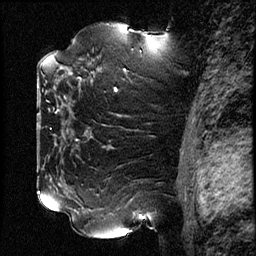
Breast MRI (dynamic contrast-enhanced), one sagittal slice; position 52 of 78 along the scan axis; dynamic contrast-enhanced study with each time point stored as its own series, time point 2 of 3 at this slice position (early post-contrast, ordered by acquisition time); 1.5 T; TE 4.2 ms, TR 17.6 ms; 256 × 256 image matrix, field of view 200 × 200 mm. Female patient, age 42 years. Case-level facts recorded for this patient, not image findings: setting: breast cancer imaged before/during neoadjuvant chemotherapy; receptor status: HER2-positive.
Outlined on this slice (semi-automatic segmentation, software-assisted and operator-edited):
- analysis volume of interest (the breast-tissue region the enhancement analysis was run in; not a lesion): bounding box (x1, y1, x2, y2) in pixels: (50, 48, 131, 129)
- tumour enhancement mask (voxels above the 100 % enhancement threshold inside the analysis volume of interest): (69, 72, 72, 74)